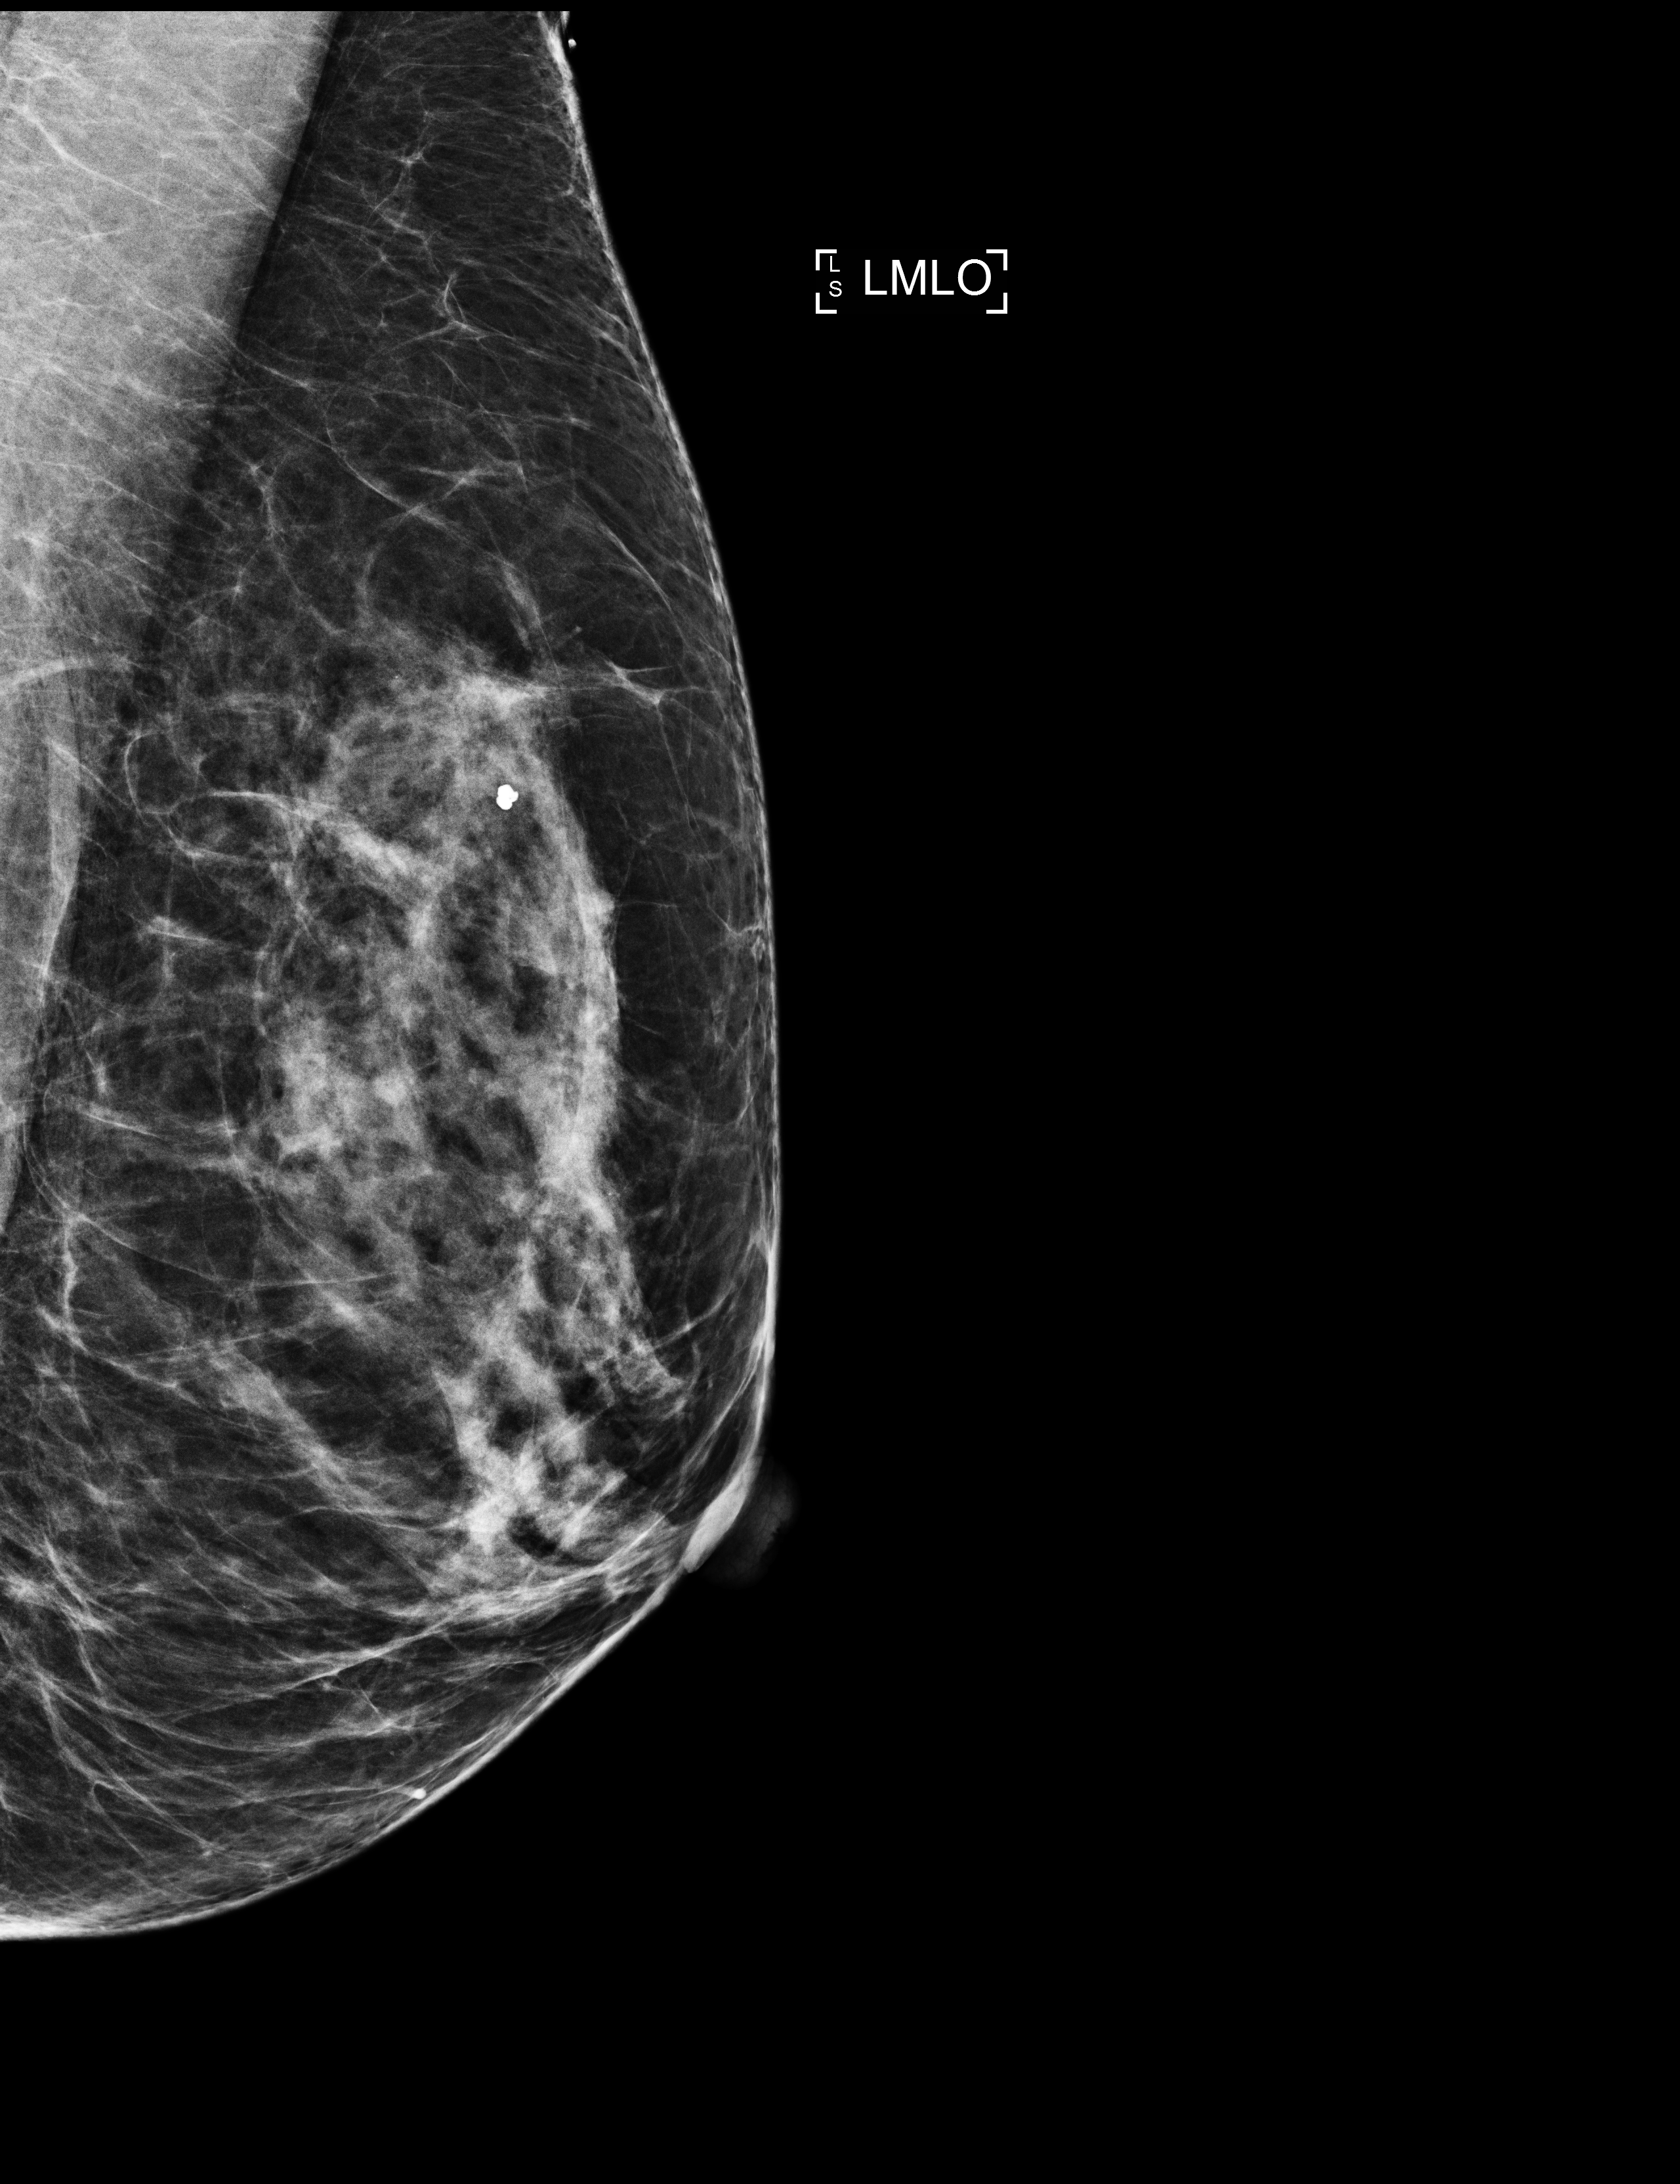
Annual screening mammography examination; system: Selenia Dimensions. Patient aged 61 years (female).
Image type: full-field digital mammogram. Breast: left. Projection: mediolateral oblique (MLO) view.